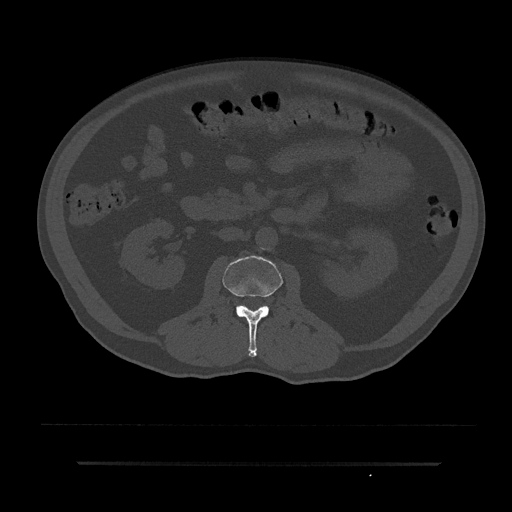
CT including the spine, one axial slice; slice 61 of 797 in the series (ordered by position); 120 kVp; bone window (W 1800 / L 400 HU); 512 × 512 image matrix, field of view 464 × 464 mm. Male patient, age 59 years. From the clinical record (not read from this slice): primary cancer: bile ducts; vertebrae with lytic lesions (as recorded): T10.
Annotated regions visible in this slice (semi-automatically segmented with operator editing):
- L2 vertebra: bounding box (x1, y1, x2, y2) in pixels: (223, 256, 283, 357)